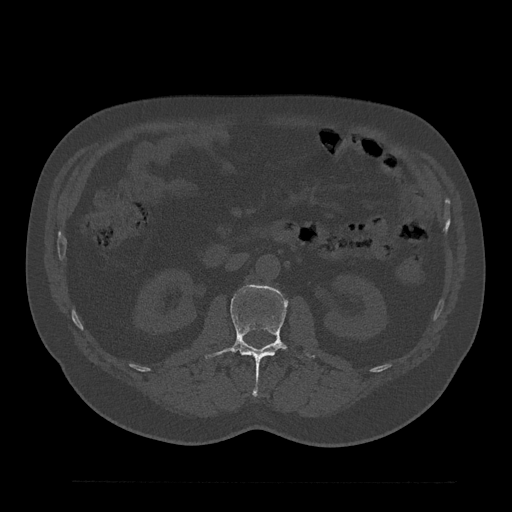
CT including the spine, one axial slice; position 98 of 797 along the scan axis; reconstruction kernel Br40s/3; 120 kVp; bone window (W 1800 / L 400 HU); 0.5 mm slice thickness; 512 × 512 image matrix, field of view 430 × 430 mm. Patient: male, 61 years. From the clinical record (not read from this slice): primary cancer: prostate.
Annotated regions visible in this slice (semi-automatic segmentation, software-assisted and operator-edited):
- L2 vertebra: box from (x=204, y=285) to (x=315, y=394) px